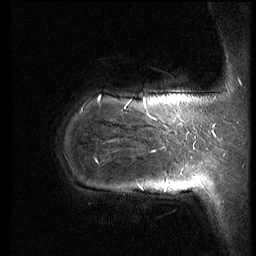
Breast MRI (dynamic contrast-enhanced), one sagittal slice; slice 15 of 66 in the series (ordered by position); dynamic contrast-enhanced series, image 2 of 3 at this slice position (ordered by acquisition); 1.5 T; TE 4.2 ms, TR 8.9 ms; 2.5 mm slice thickness; 256 × 256 image matrix, field of view 200 × 200 mm. Female patient, age 39 years. Case-level facts recorded for this patient, not image findings: setting: breast cancer imaged before/during neoadjuvant chemotherapy; receptor status: HER2-positive.
Structures marked on this image (semi-automatically segmented with operator editing):
- analysis volume of interest (the breast-tissue region the enhancement analysis was run in; not a lesion): box from (x=56, y=75) to (x=188, y=218) px
- tumour enhancement mask (voxels above the 140 % enhancement threshold inside the analysis volume of interest): (x=96, y=96)–(x=158, y=163)